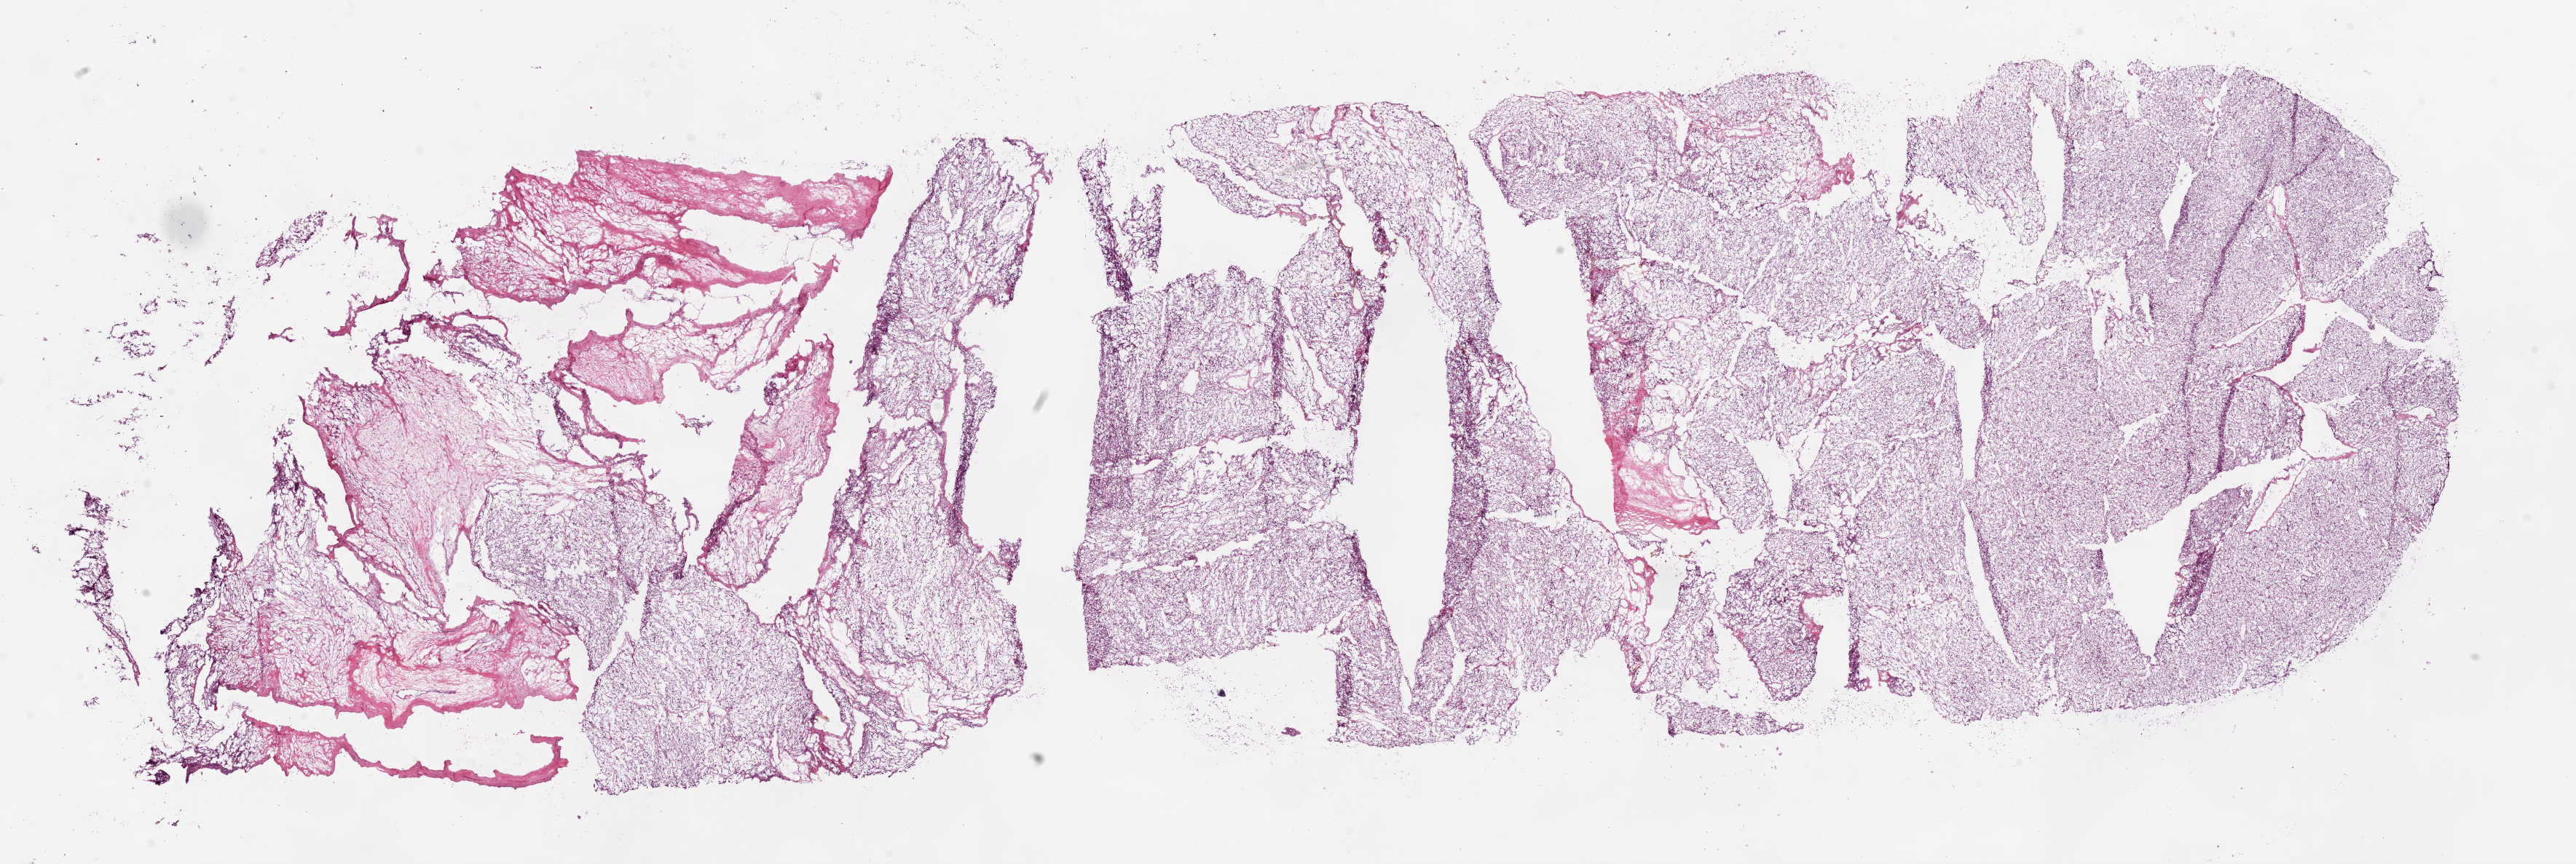
H&E whole-slide image — low-resolution overview of the scanned area, about 28.5 x 9.6 mm (from a 20x scan), frozen section from the bottom of the tissue portion, sample: primary tumour, kidney. Male patient; age at initial diagnosis 61 years. Histologic grade: G2 (moderately differentiated). Slide review estimates, as recorded: tumour cells 80%, tumour nuclei 85%, normal cells 0%, stromal cells 20%, necrosis 0%.
* diagnosis: Clear cell adenocarcinoma, NOS
* AJCC pathologic stage: III